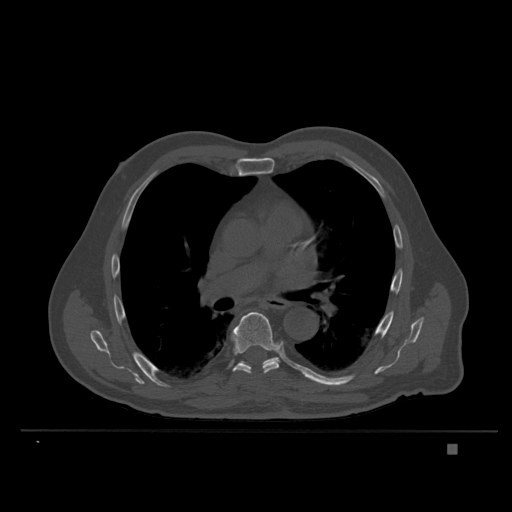
CT including the spine, one axial slice. Position 243 of 435 along the scan axis. Bone window (W 1800 / L 400 HU). 1.5 mm slice thickness. 512 × 512 image matrix, field of view 434 × 434 mm. Patient: male, 73 years. From the clinical record (not read from this slice): primary cancer: skin.
Annotated regions visible in this slice (semi-automatic segmentation, software-assisted and operator-edited):
- T7 vertebra: bounding box <230,312,281,374> (left, top, right, bottom; pixels)
- T8 vertebra: <239,357,279,366>